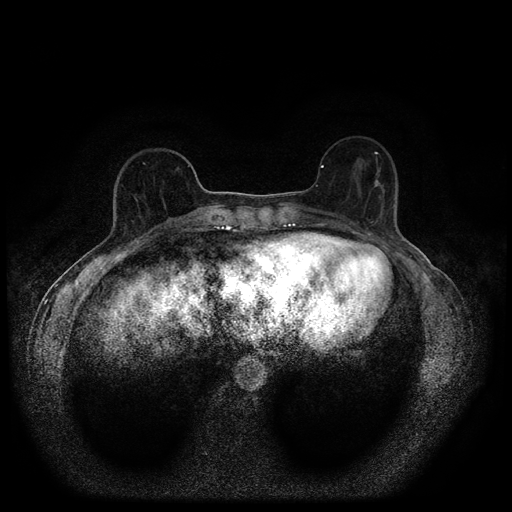
Breast MRI (dynamic contrast-enhanced, multi-phase), one axial slice; slice 33 of 116 in the series (ordered by position); dynamic contrast-enhanced series, time point 2 of 5 at this slice position (early post-contrast); 1.5 T; TE 2.7 ms, TR 5.4 ms; 2 mm slice thickness; 512 × 512 image matrix, field of view 330 × 330 mm. Patient: female, 56 years.
Outlined on this slice (semi-automatically segmented with operator editing):
- breast lesion (labelled 'tumour' in the annotation; benign lesions carry a separate 'benign' label): bounding box (x1, y1, x2, y2) in pixels: (372, 157, 383, 188)